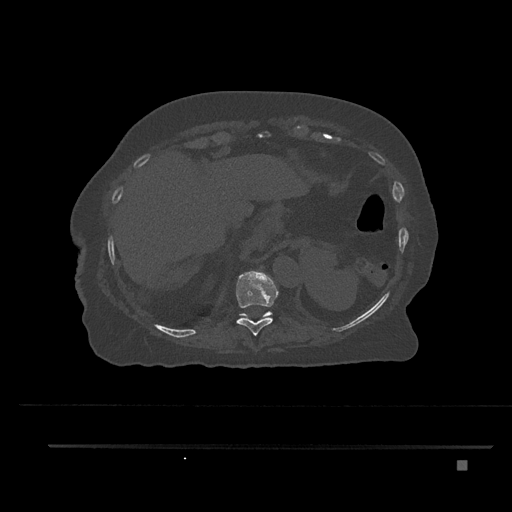
CT including the spine, one axial slice. Slice 347 of 797 in the series (ordered by position). Bone window (W 1800 / L 400 HU). 0.5 mm slice thickness. 512 × 512 image matrix, field of view 437 × 437 mm. Patient: female, 76 years. Case-level facts recorded for this patient, not image findings: primary cancer: lung.
Outlined on this slice (semi-automatic segmentation, software-assisted and operator-edited):
- T10 vertebra: box from (x=225, y=270) to (x=278, y=336) px
- T11 vertebra: (x=240, y=311)–(x=272, y=319)